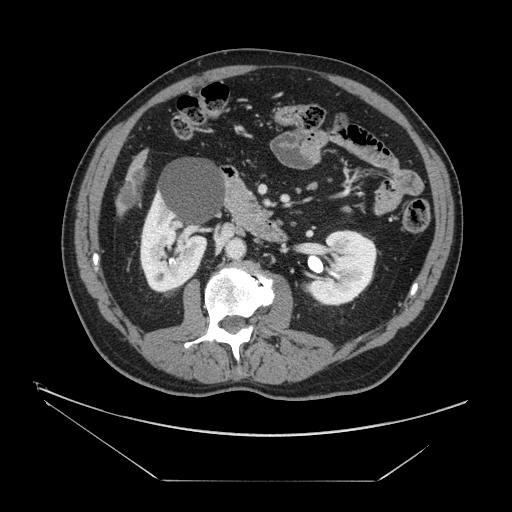
Contrast-enhanced abdominal CT, one axial slice. Position 49 of 161 along the scan axis. Reconstruction kernel STANDARD. Intravenous contrast given. Soft-tissue window (W 400 / L 40 HU). 2.5 mm slice thickness. 512 × 512 image matrix, field of view 440 × 440 mm. Male patient, age 65 years. Case-level facts recorded for this patient, not image findings: diagnosis: colorectal cancer liver metastases, imaged before liver resection; multiple liver metastases: yes; largest metastasis: 4.2 cm; disease in both lobes: yes.
Structures marked on this image (expert manual segmentation):
- liver: bounding box <122,159,143,207> (left, top, right, bottom; pixels)
- liver metastasis: <120,173,142,207>